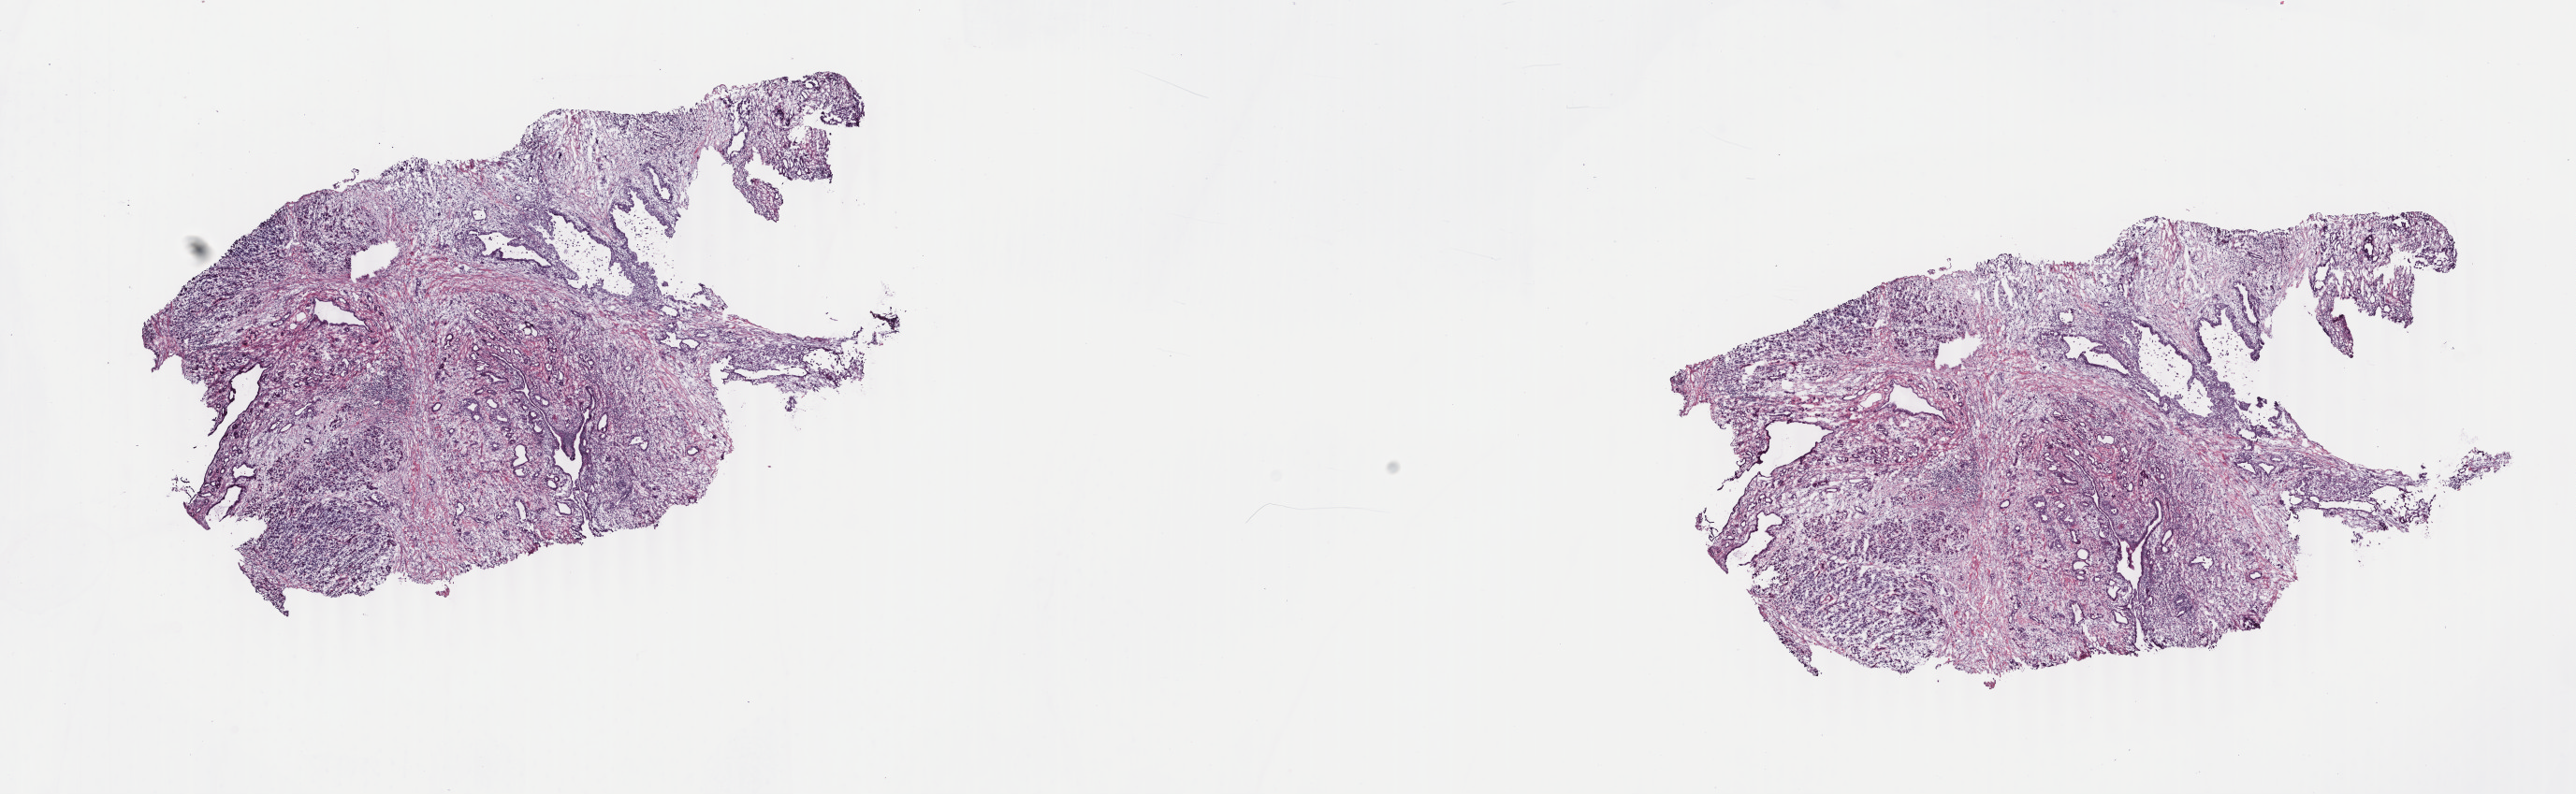
Whole-slide histology image, Hematoxylin and eosin (H&E) stained, whole scanned area (about 21.9 x 6.8 mm, acquisition: 40x scan) shown as a low-resolution overview; frozen section from the top of the tissue portion; sample: primary tumour, pancreas. Male patient; age at initial diagnosis 72 years. Pathologist review of this section (percent, as recorded): tumour cells 30%, tumour nuclei 45%.
Diagnosis: Adenocarcinoma, NOS (head of pancreas).